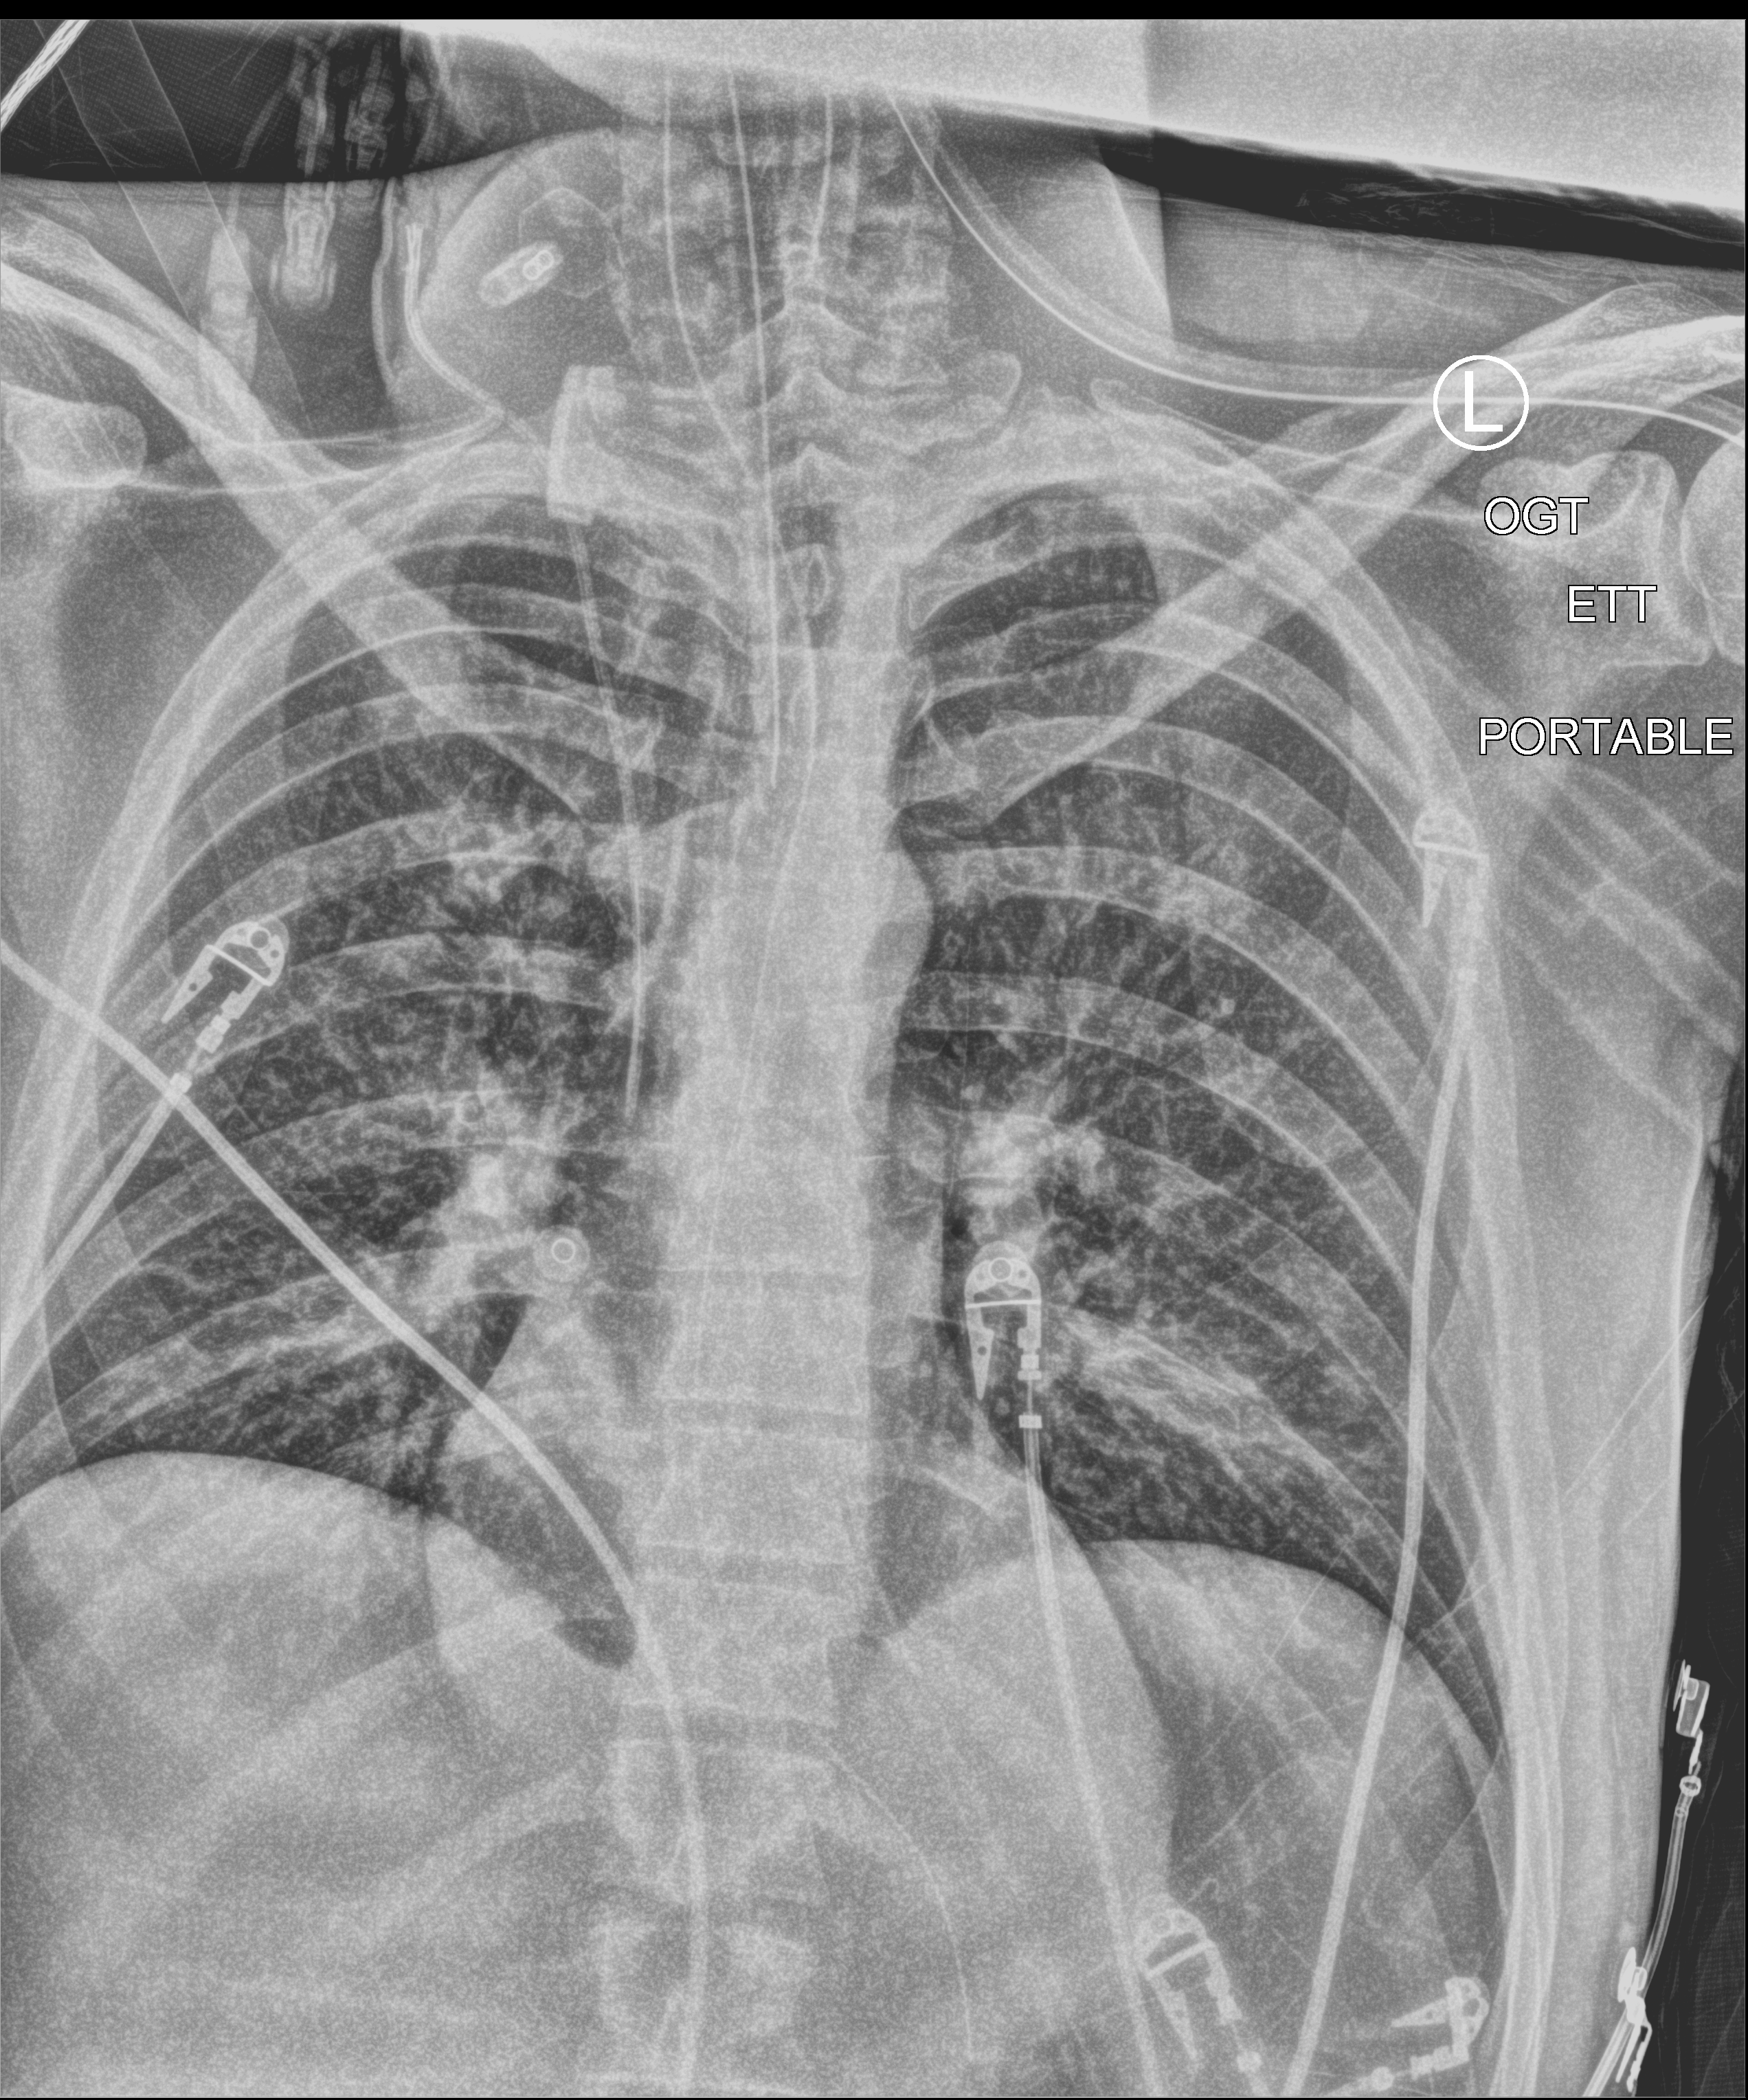
Chest X-ray (portable); anteroposterior (AP) projection. Patient hospitalised with COVID-19; male, aged 18–59 years.
Hospital-stay facts (about this admission, not read from this image; timing relative to this image not recorded): mechanically ventilated during this hospital stay: yes; length of hospital stay: 4 days.